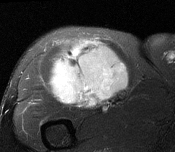
MRI of an extremity soft-tissue mass, one axial slice; slice 102 of 116 in the series (ordered by position); T2-weighted fat-saturated; MR volume resampled by the dataset authors to the PET/CT grid (not the native acquisition matrix); 3.27 mm slice thickness; 175 × 152 image matrix, field of view 171 × 148 mm. Male patient. From the clinical record (not read from this slice): histological type: pleiomorphic leiomyosarcoma; grade: intermediate; site of the primary tumour: right thigh.
Annotated regions visible in this slice (expert contour drawn on MRI and transferred to this co-registered scan by the dataset authors):
- gross tumour volume including surrounding oedema: bounding box <51,40,130,107> (left, top, right, bottom; pixels)
- gross tumour volume (mass): <51,40,130,107>